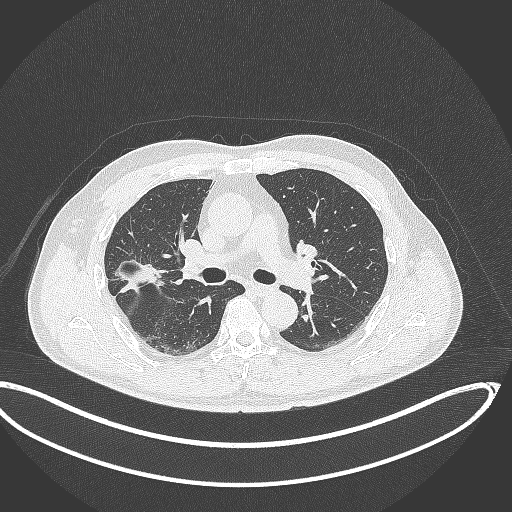
Chest CT, one axial slice. Slice 206 of 391 in the series (ordered by position). Reconstruction kernel B70f. 120 kVp. Lung window (W 1500 / L -600 HU). 1 mm slice thickness. 512 × 512 image matrix, field of view 439 × 439 mm. Patient: male, 63 years. From the clinical record (not read from this slice): clinical TNM (as recorded): T1c N0 M0; histopathological grade: G2-3.
Annotated regions visible in this slice (rectangle marked by the reading radiologist):
- lung tumour (recorded histology: adenocarcinoma): bounding box [x1, y1, x2, y2] px = [111, 254, 169, 302]